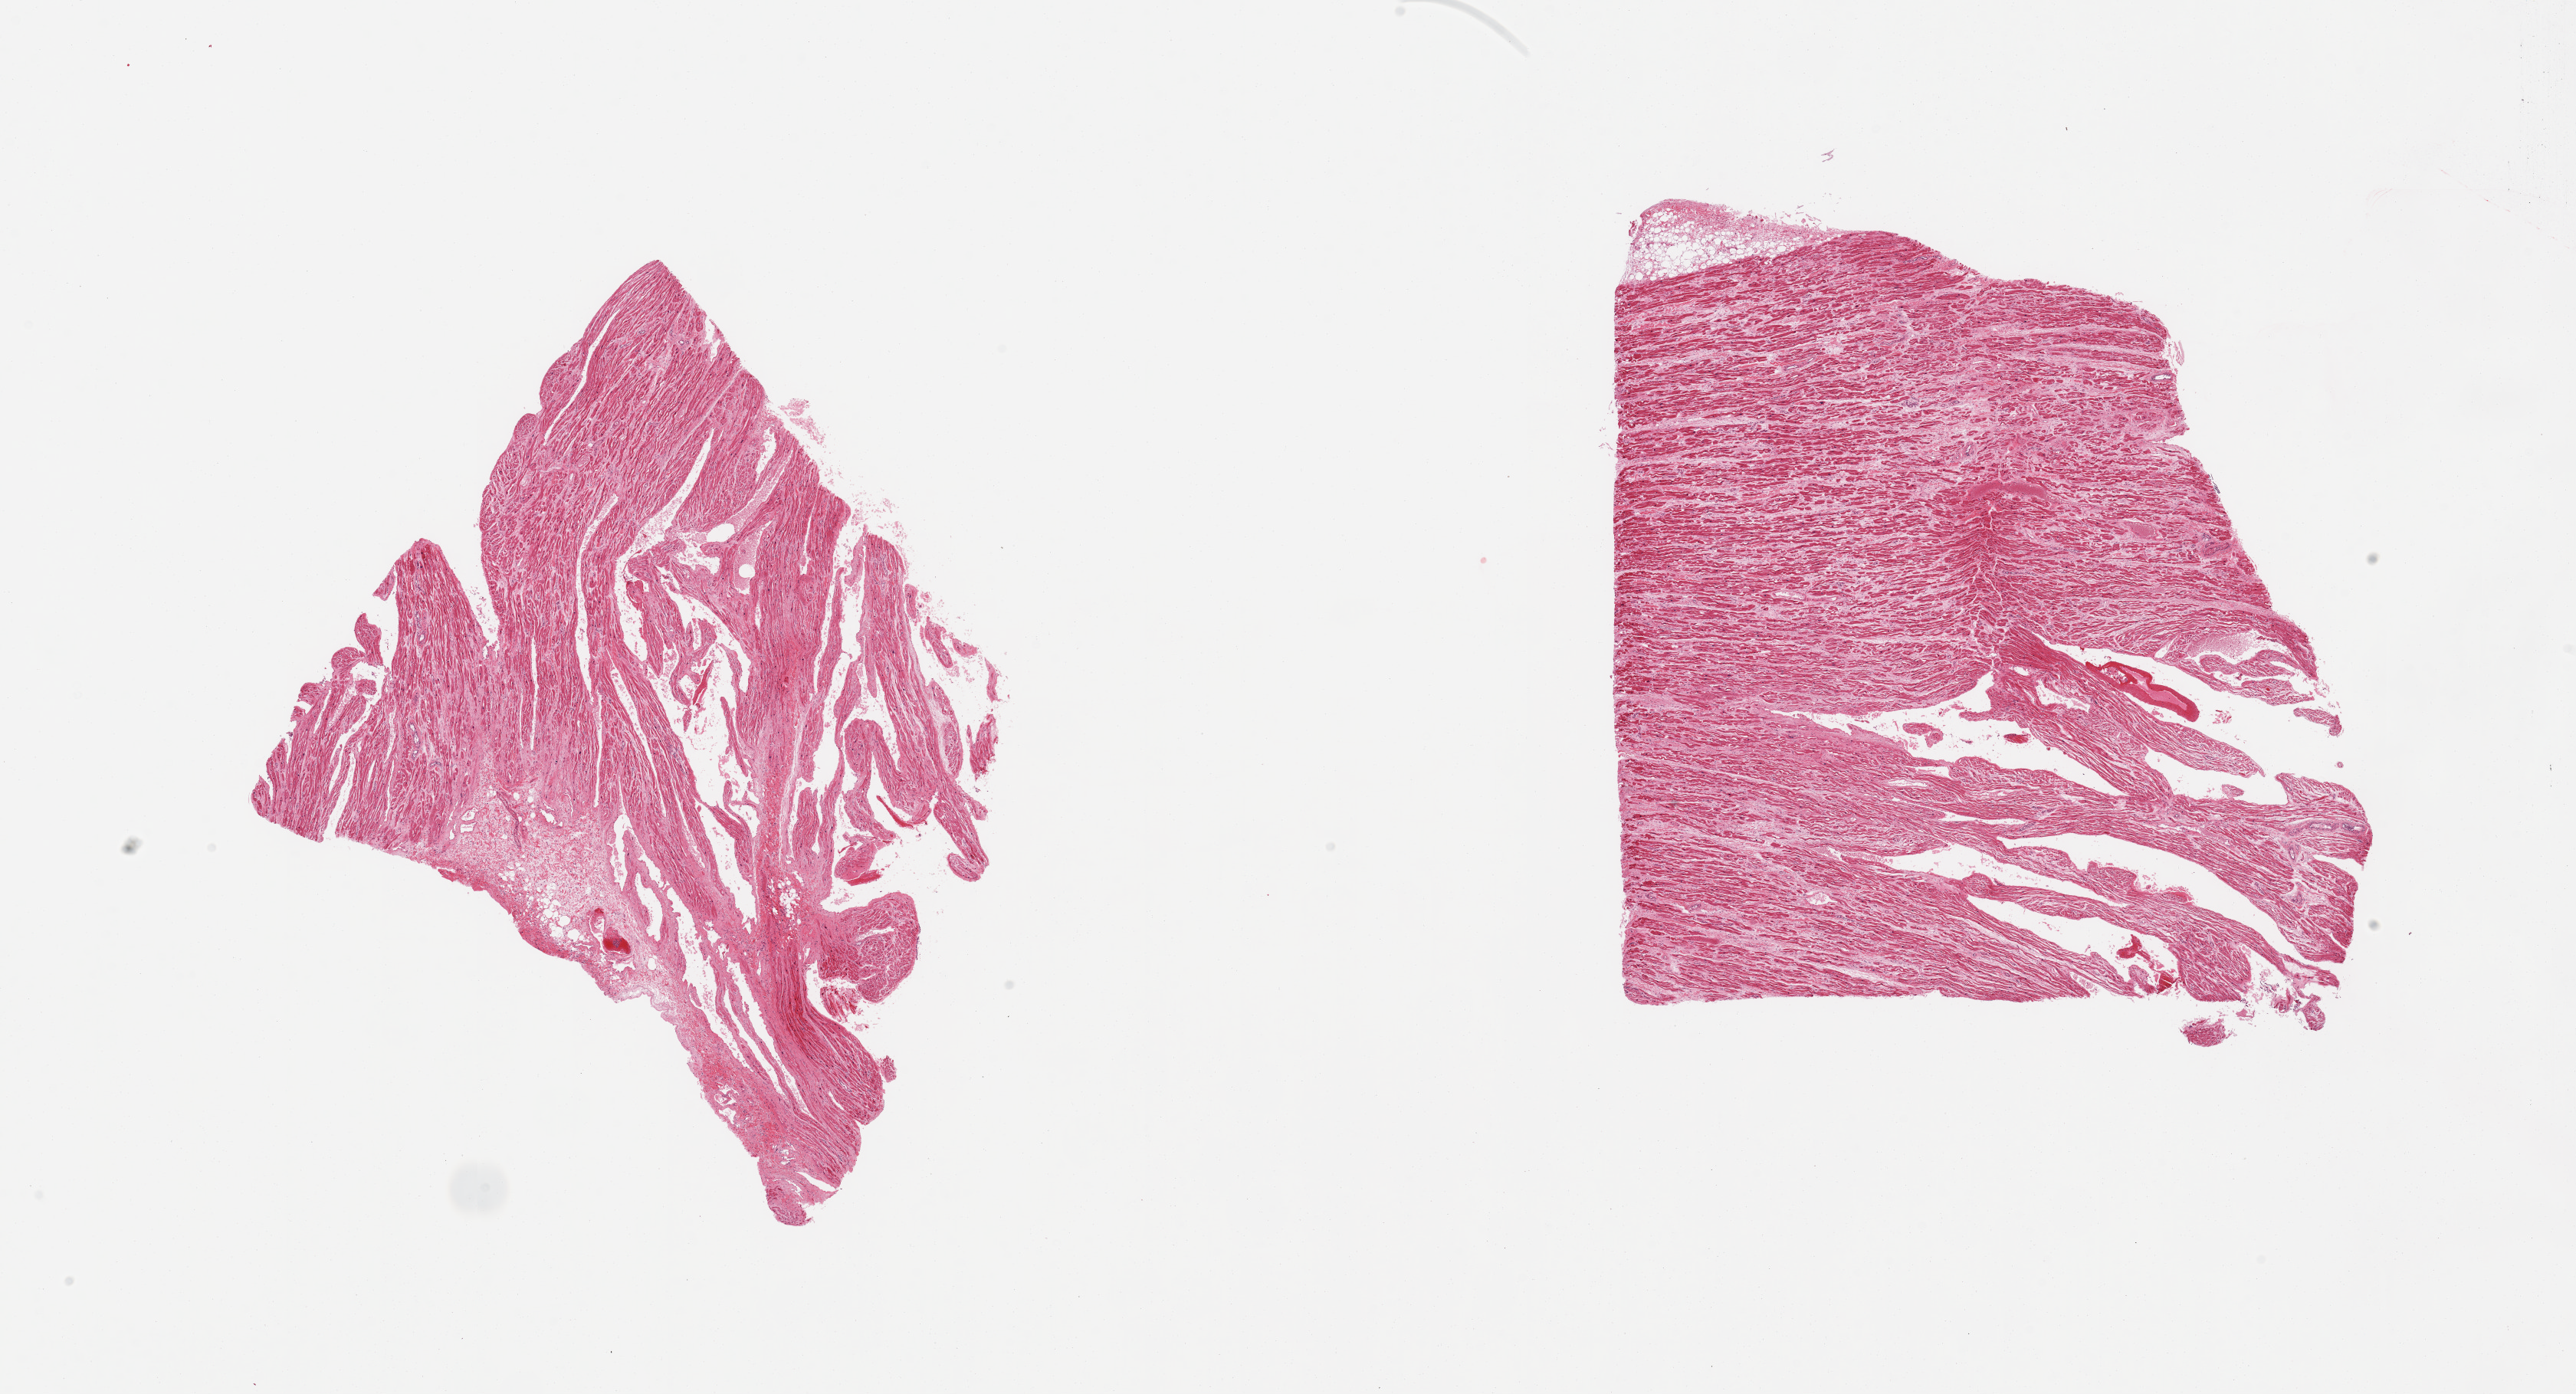
Whole-slide image, haematoxylin and eosin stain — shown as a low-resolution overview of the whole scanned area (about 26.6 x 14.4 mm, slide scanned at 20x). PAXgene-fixed, paraffin-embedded tissue. Target tissue: auricular appendage. Donor tissue sample. Male donor.
* pathologist's review note for this sample: 2 pieces; small amount of external fat, hypertrophy, some interstitial fibrosis